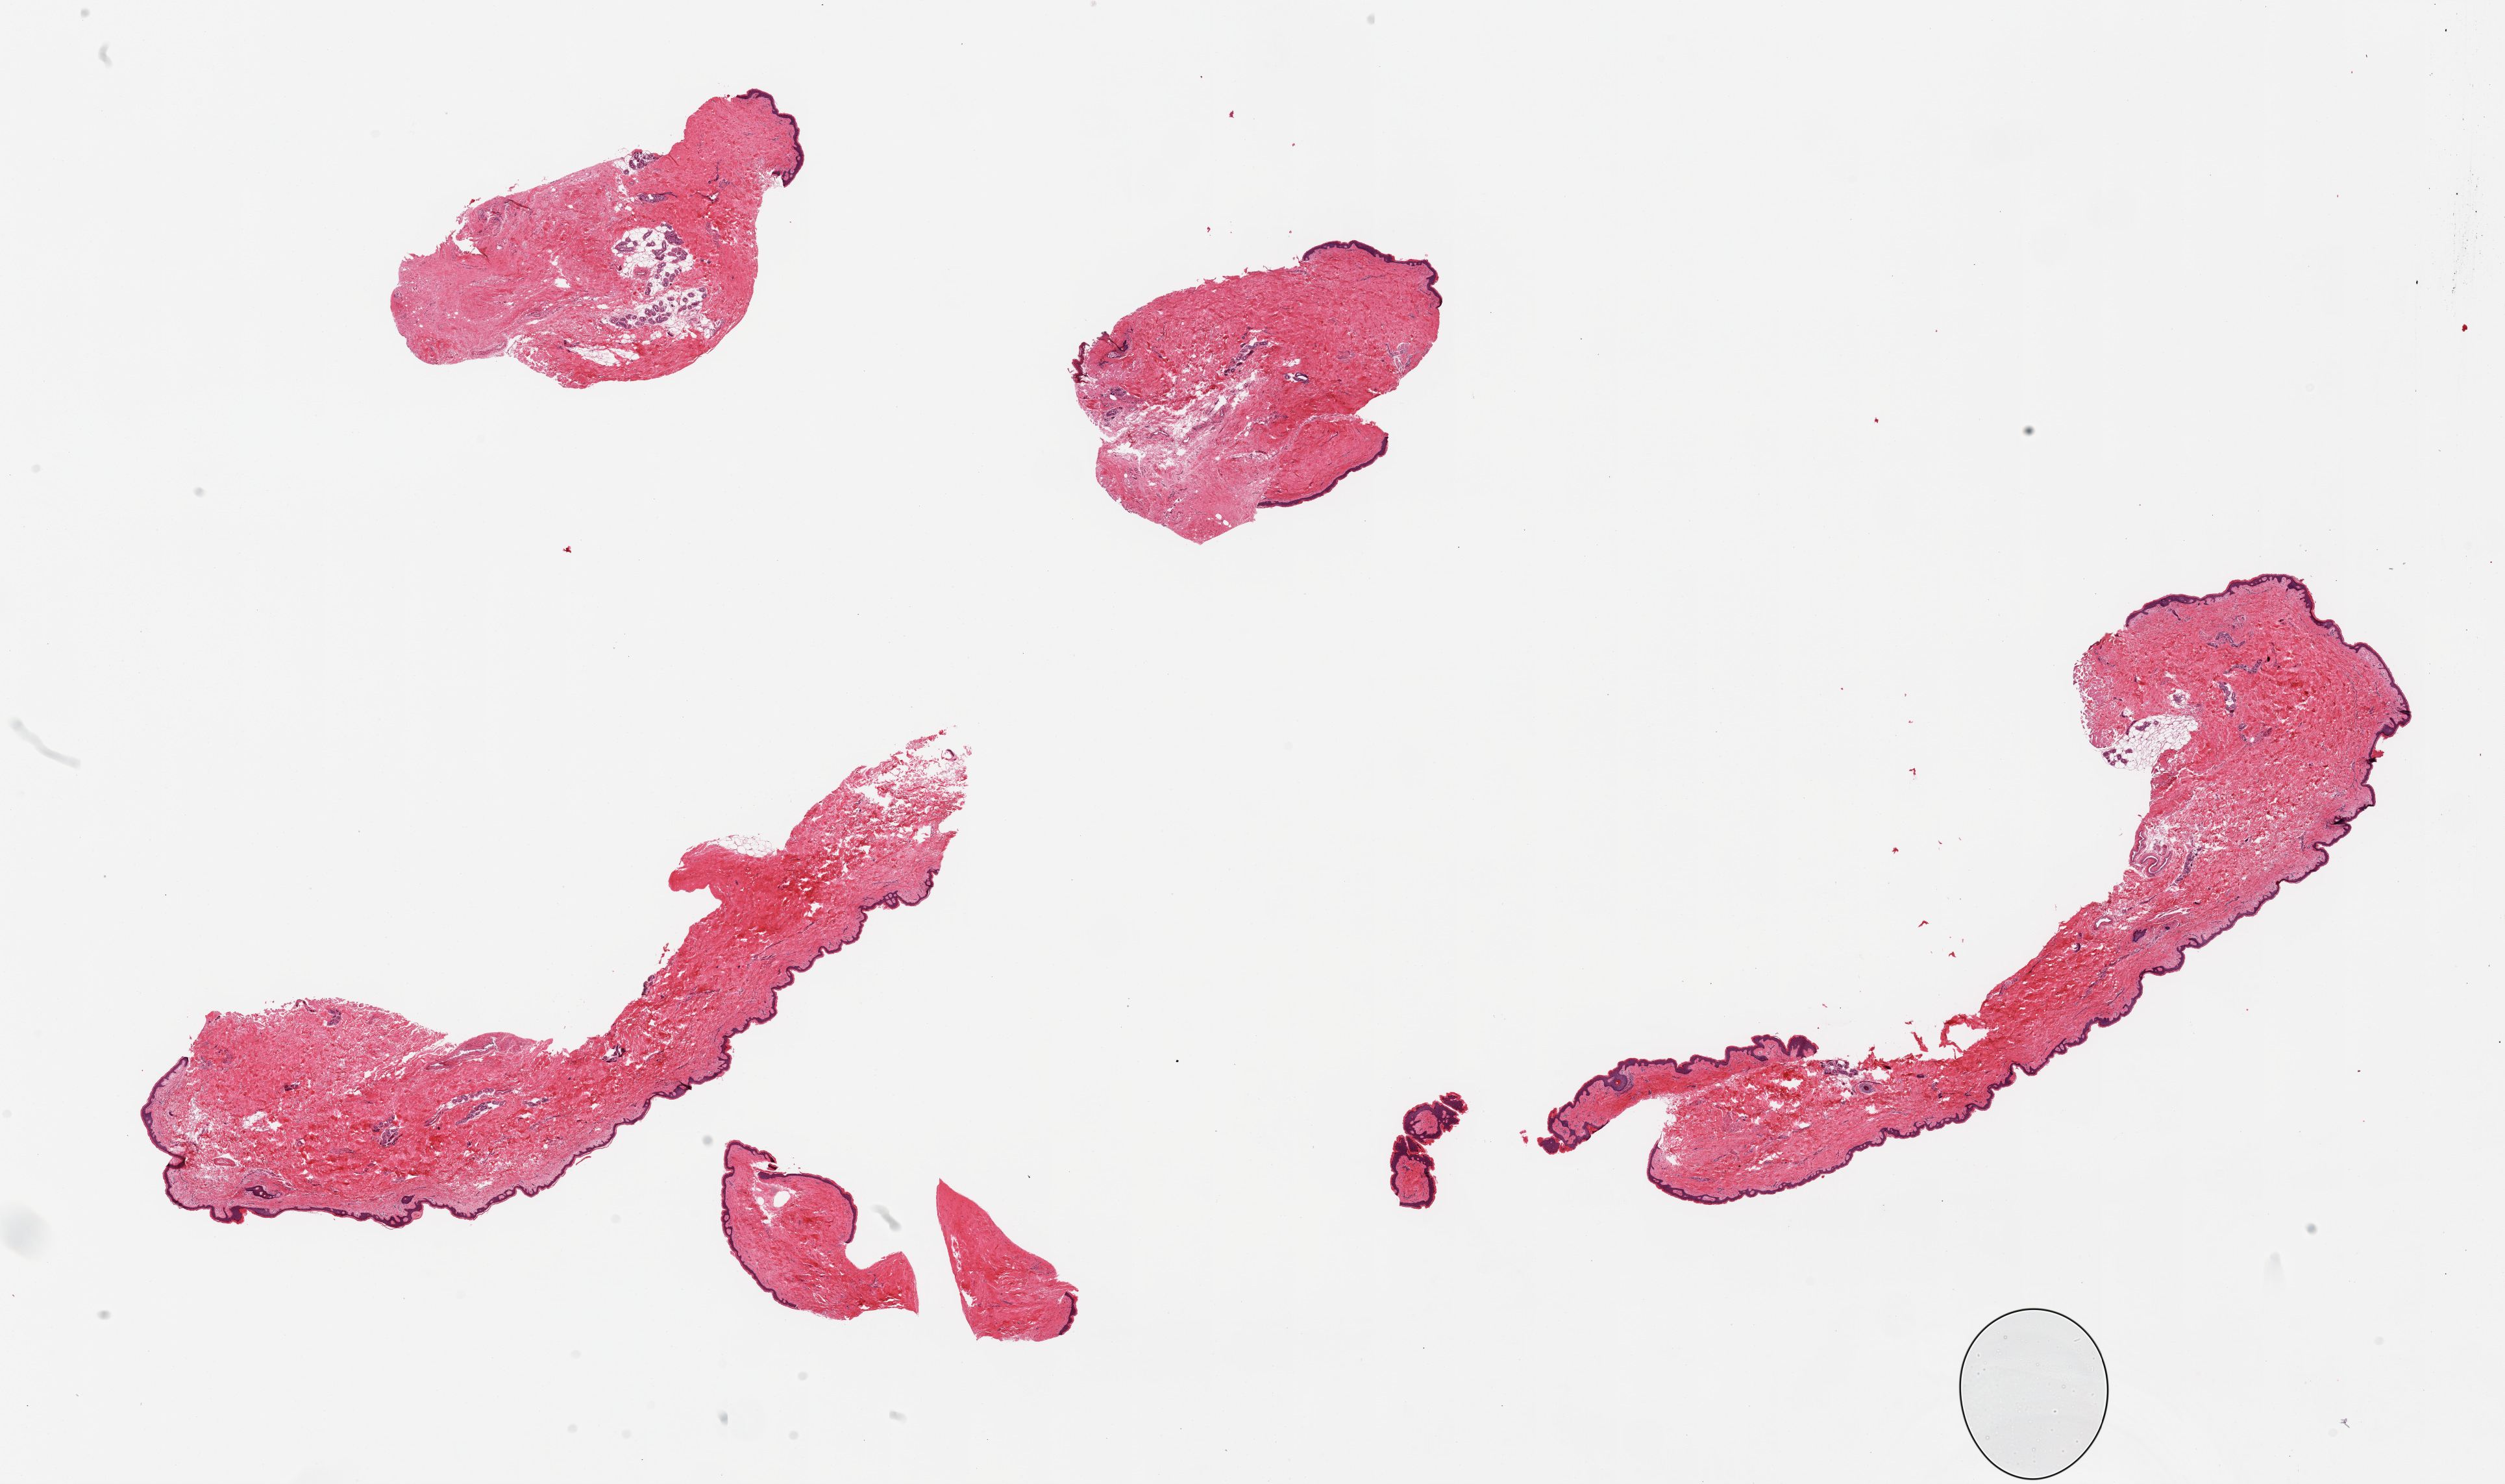
Digitized H&E-stained section, brightfield, whole scanned area (about 30.5 x 18.1 mm) shown as a low-resolution overview, PAXgene-fixed paraffin-embedded (PFPE) section, section of skin of suprapubic region (target tissue), tissue donor sample. Female donor.
Reviewer comment on this tissue sample: 5 pieces; well trimmed.